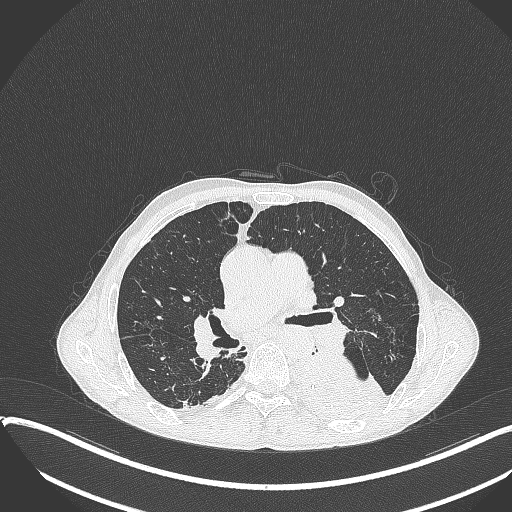
Chest CT, one axial slice; slice 220 of 401 in the series (ordered by position); 120 kVp; lung window (W 1500 / L -600 HU); 1 mm slice thickness; 512 × 512 image matrix, field of view 400 × 400 mm. Patient: male, 57 years. From the clinical record (not read from this slice): clinical TNM (as recorded): T4 N0 M0.
Structures marked on this image (bounding box drawn by a radiologist):
- lung tumour (recorded histology: squamous cell carcinoma): bounding box [x1, y1, x2, y2] px = [288, 356, 386, 427]